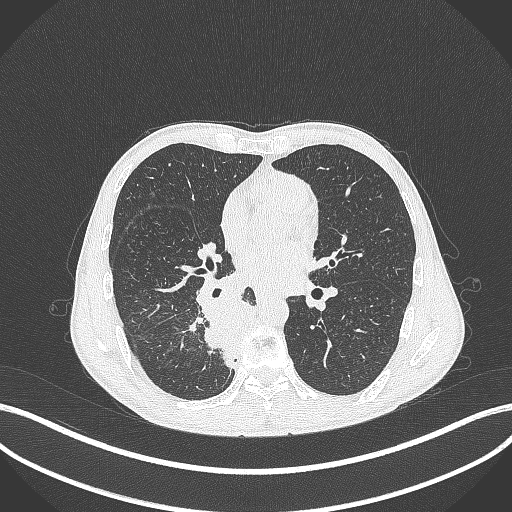
Chest CT, one axial slice; position 185 of 371 along the scan axis; reconstruction kernel B70f; lung window (W 1500 / L -600 HU); 1 mm slice thickness; 512 × 512 image matrix, field of view 400 × 400 mm. Patient: male, 58 years. Case-level facts recorded for this patient, not image findings: clinical TNM (as recorded): T3 N1 M1.
Annotated regions visible in this slice (rectangle marked by the reading radiologist):
- lung tumour (recorded histology: squamous cell carcinoma): box from (x=190, y=289) to (x=273, y=373) px